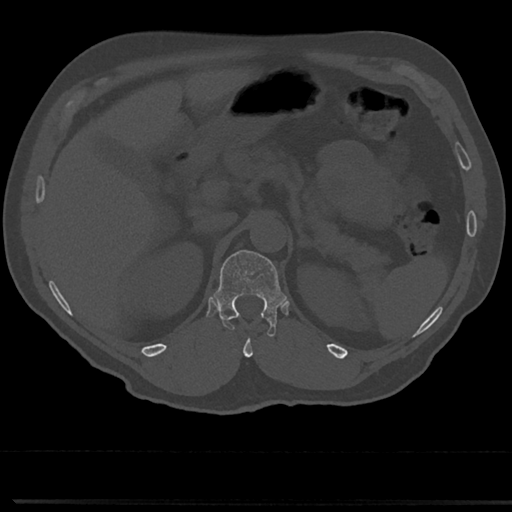
CT including the spine, one axial slice; slice 159 of 817 in the series (ordered by position); reconstruction kernel Br40s/3; bone window (W 1800 / L 400 HU); 0.5 mm slice thickness; 512 × 512 image matrix, field of view 355 × 355 mm. Male patient, age 61 years. From the clinical record (not read from this slice): primary cancer: prostate.
Structures marked on this image (semi-automatic segmentation, software-assisted and operator-edited):
- T12 vertebra: bounding box <216,248,282,334> (left, top, right, bottom; pixels)